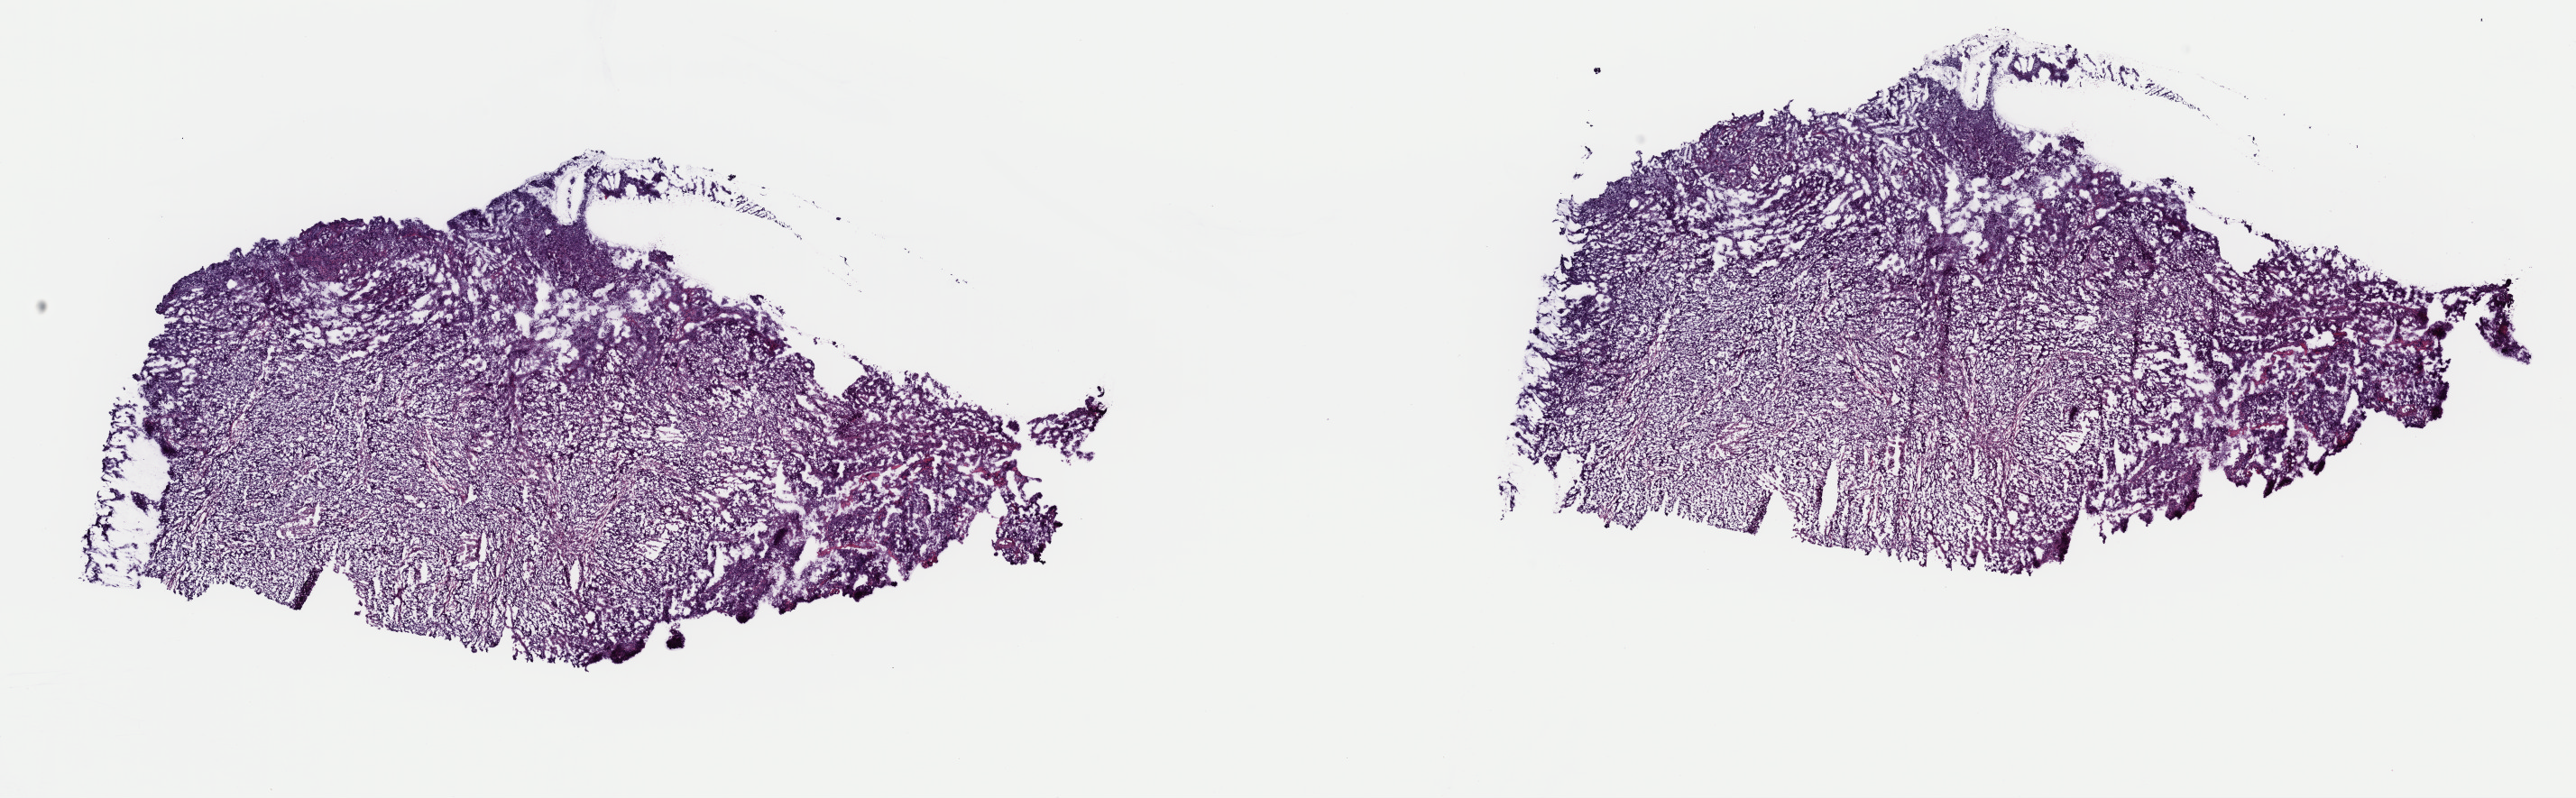
Digitized H&E-stained tissue section (whole slide) — a low-resolution overview of the entire scanned area, about 22.6 x 7.0 mm (slide scanned at 40x); frozen section; cervix, primary tumour sample. Female, age 44 years at initial diagnosis. Pathologist review of this section (percent, as recorded): tumour cells 100%, tumour nuclei 80%.
Histologic diagnosis: Squamous cell carcinoma, NOS (cervix uteri).